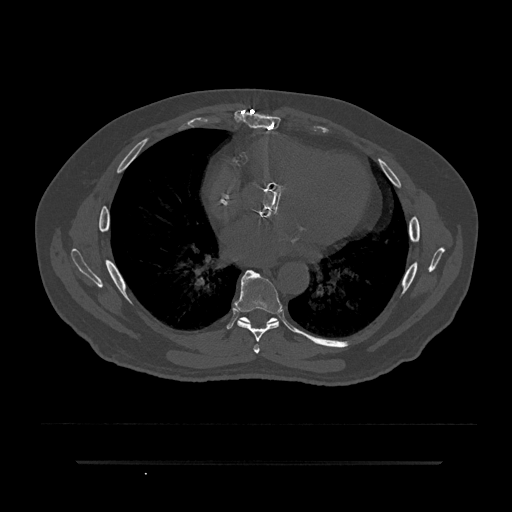
CT including the spine, one axial slice; slice 465 of 797 in the series (ordered by position); reconstruction kernel Br40s/3; bone window (W 1800 / L 400 HU); 0.5 mm slice thickness; 512 × 512 image matrix, field of view 464 × 464 mm. Male patient, age 59 years. From the clinical record (not read from this slice): primary cancer: bile ducts.
Annotated regions visible in this slice (semi-automatic segmentation, software-assisted and operator-edited):
- T6 vertebra: box from (x=253, y=344) to (x=260, y=354) px
- T7 vertebra: (x=234, y=270)–(x=282, y=342)
- T8 vertebra: (x=238, y=317)–(x=297, y=333)